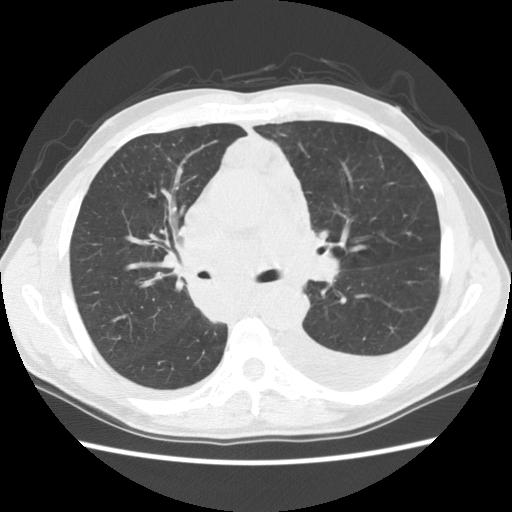
Chest CT (low-dose screening protocol), one axial image. First (baseline) screen. Lung window (W 1500 / L -600 HU). 2.5 mm slice thickness. Slice 46 of 135 in the series. 512 × 512 image matrix. Male participant, aged 60 years at enrolment. Current smoker at enrolment.
• Lesion marked by an expert reader, bounding box [x1, y1, x2, y2] px = [177, 237, 294, 327].
• No non-calcified nodule or mass ≥4 mm was recorded by the screening reader at this exam.
• Participant outcome: lung cancer diagnosed 12 days after this screen — squamous cell carcinoma, NOS, carina, poorly differentiated (G3), stage IV (AJCC 6th edition).